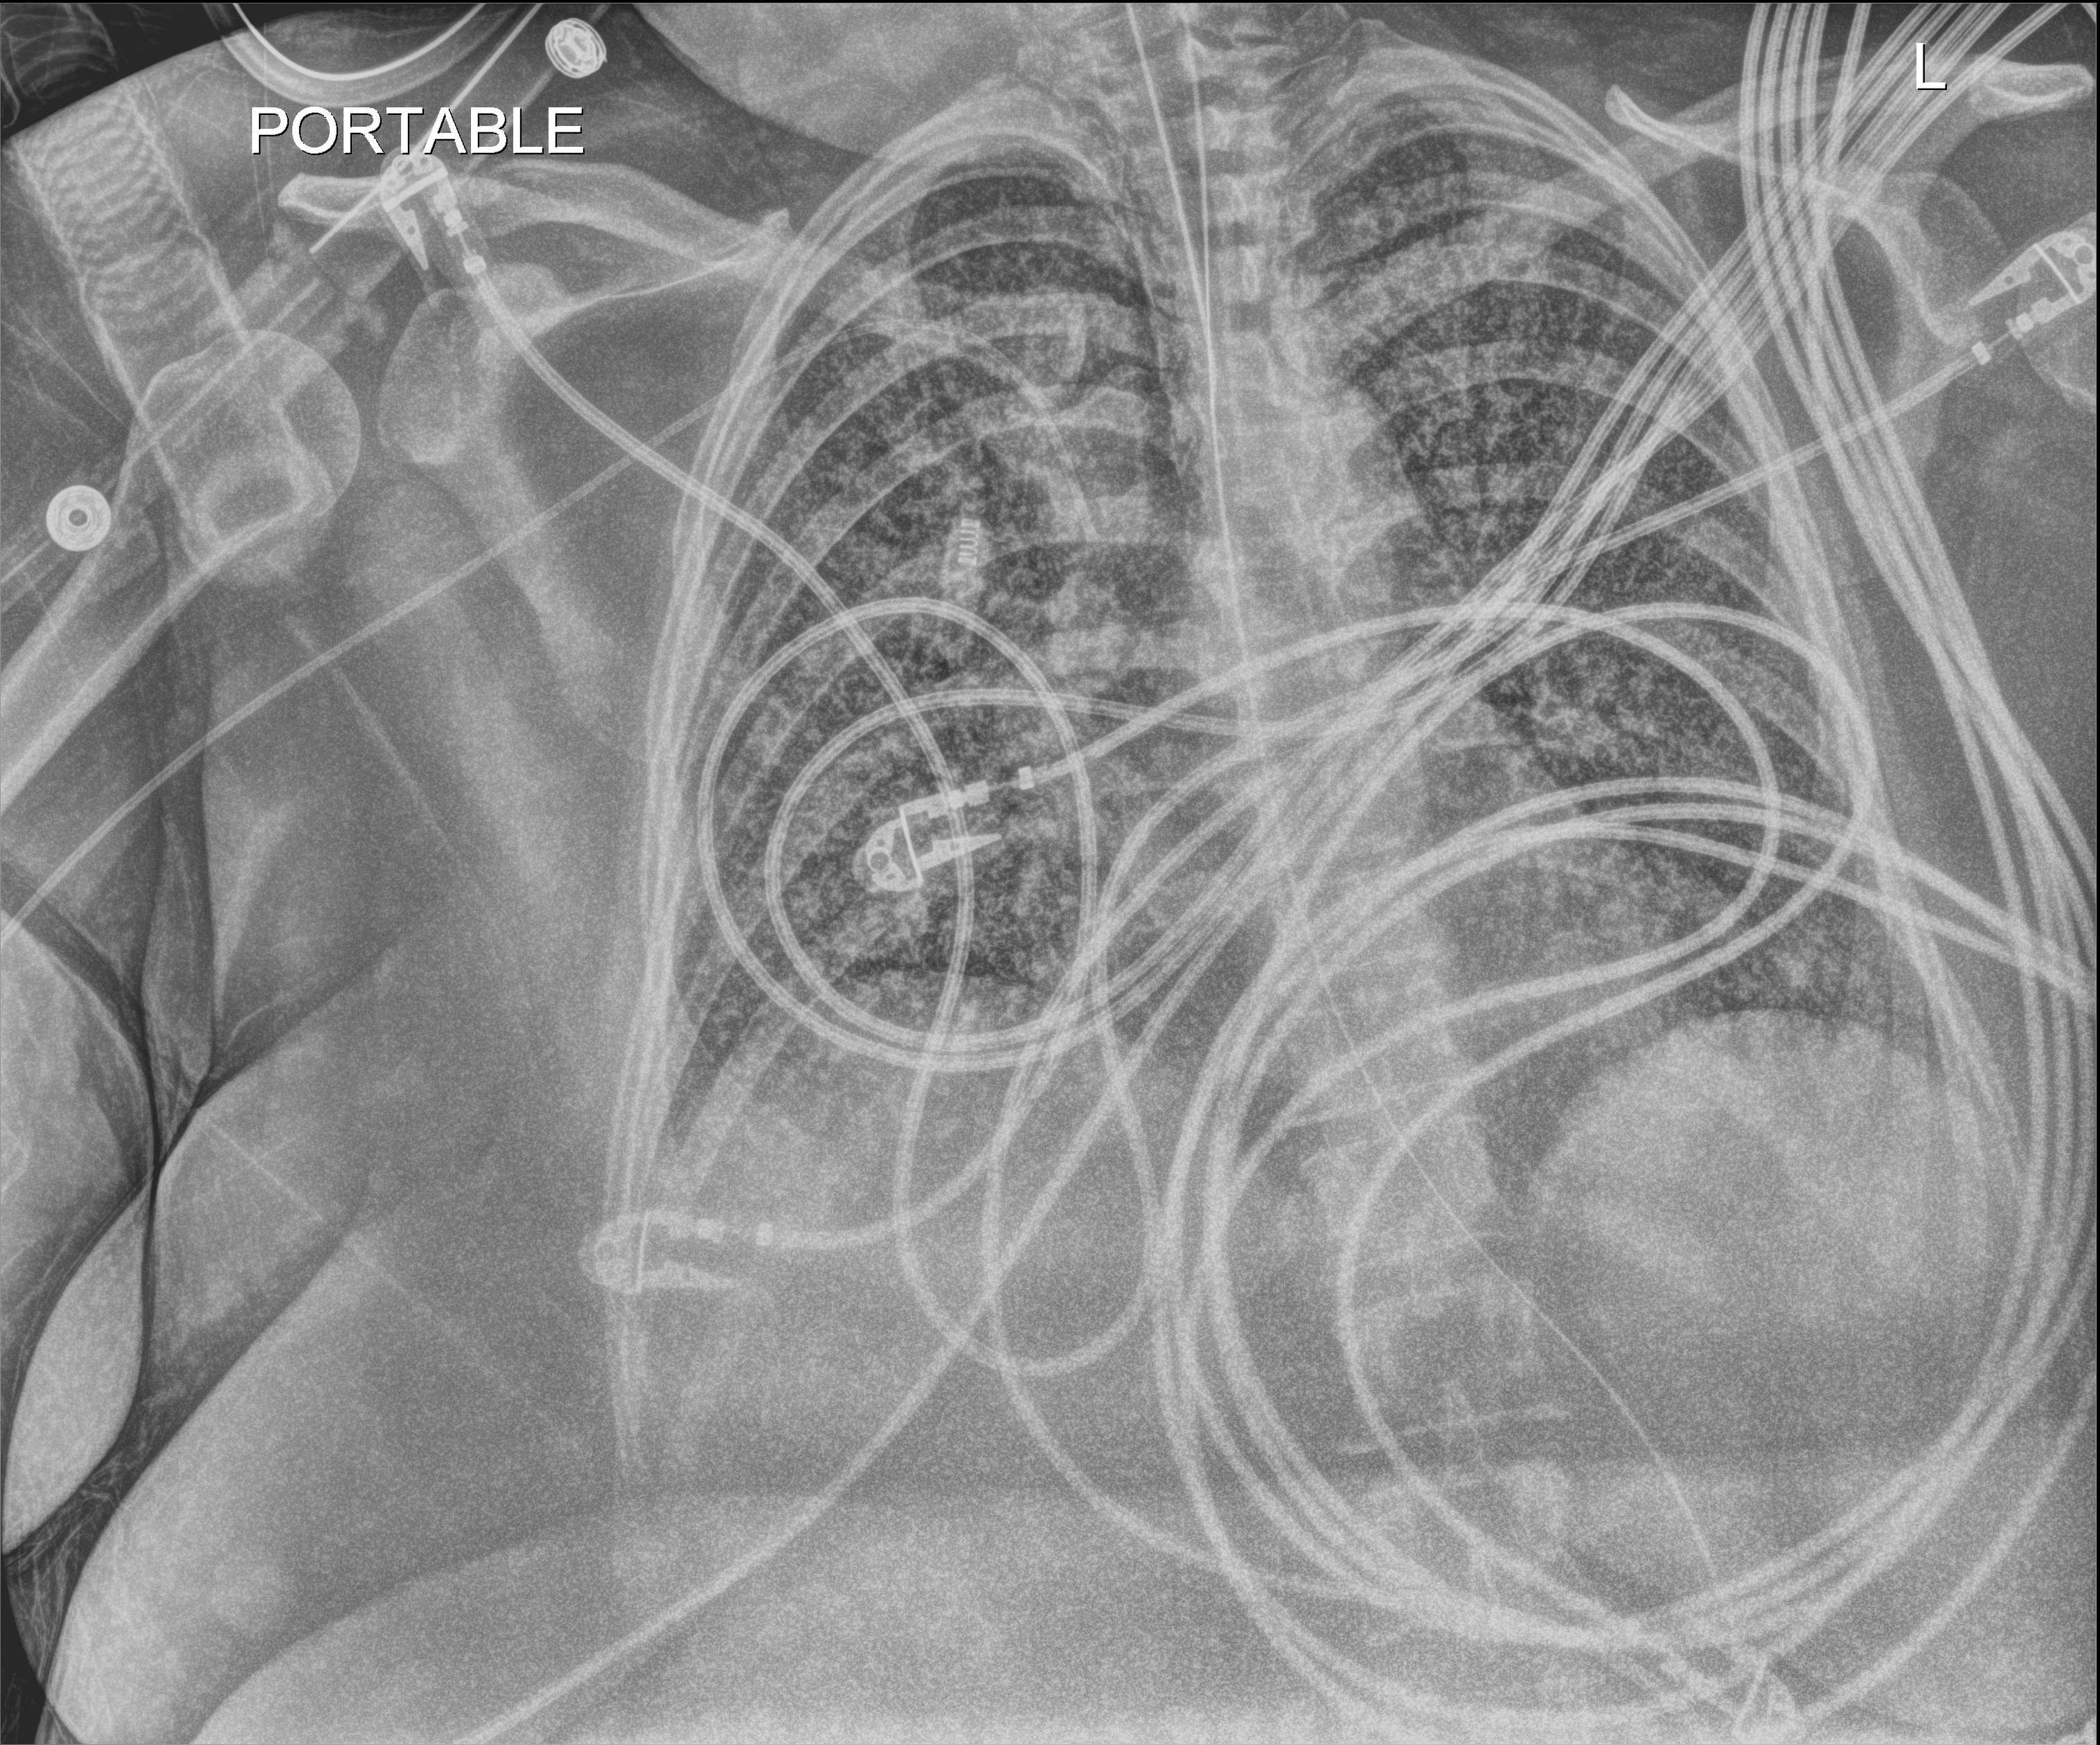
Portable chest radiograph, anteroposterior (AP) projection. Patient hospitalised with COVID-19; female, aged 18–59 years.
Admission-level facts for this patient (not findings on this image; timing relative to this image not recorded): chronic kidney disease (admission record): no; admitted to intensive care during this hospital stay: yes.